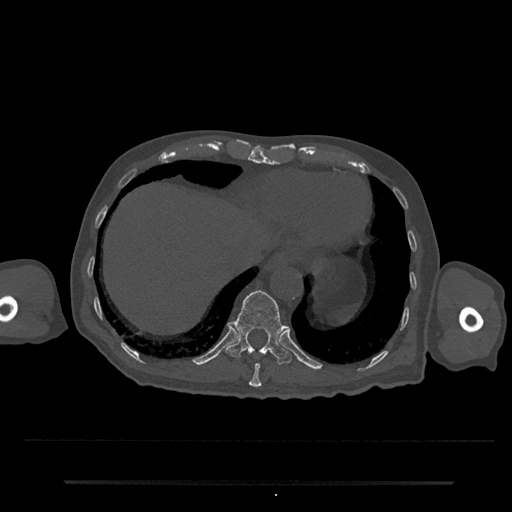
CT including the spine, one axial slice. Slice 269 of 797 in the series (ordered by position). Reconstruction kernel Br40s/3. Bone window (W 1800 / L 400 HU). 512 × 512 image matrix, field of view 427 × 427 mm. Male patient, age 74 years. Case-level facts recorded for this patient, not image findings: primary cancer: prostate.
Outlined on this slice (semi-automatic segmentation, software-assisted and operator-edited):
- T10 vertebra: bounding box <249,363,262,388> (left, top, right, bottom; pixels)
- T11 vertebra: <225,290,292,365>